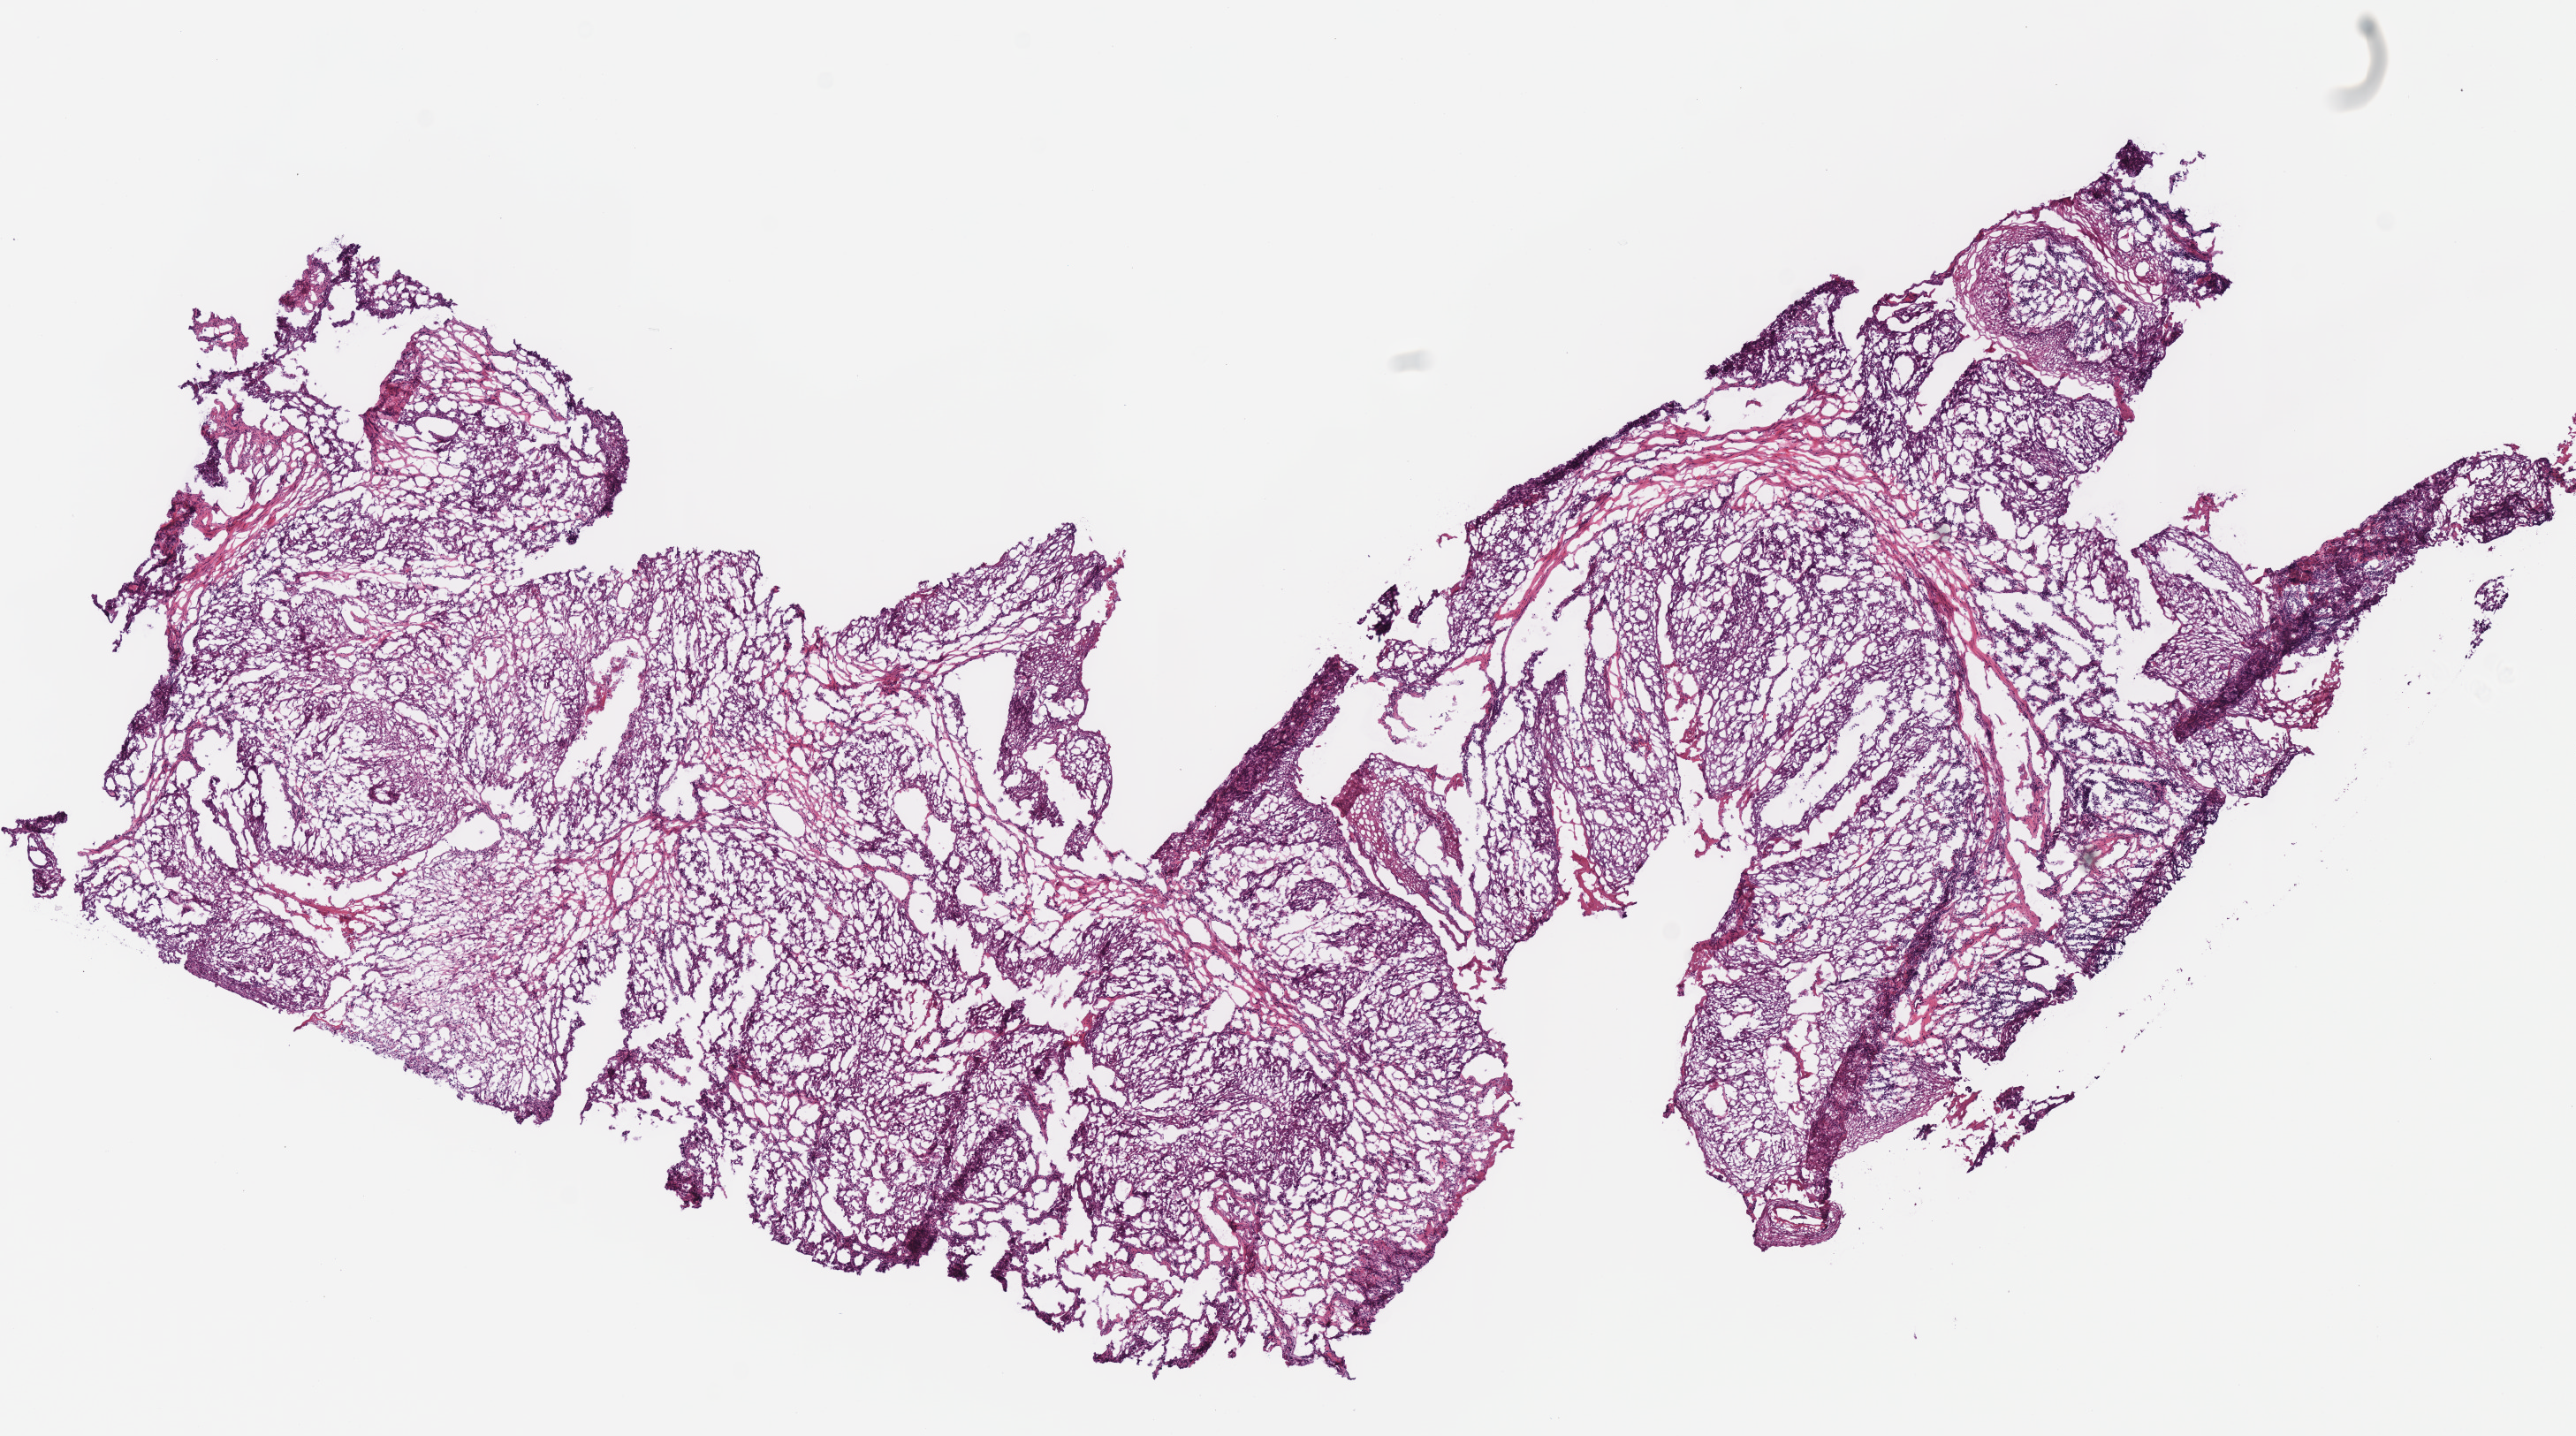
Whole-slide histology image, H&E-stained, a low-resolution overview of the entire scanned area, about 11.5 x 6.4 mm (slide scanned at 40x), frozen section from the bottom of the tissue portion, sample: primary tumour, head and neck. Male patient; age at initial diagnosis 65 years. Histologic grade: G3 (poorly differentiated). Composition of this section per pathologist review: tumour cells 85%, tumour nuclei 71%, normal cells 15%, stromal cells 0%, necrosis 0%. Inflammatory infiltration, as recorded: lymphocyte infiltration 10%, monocyte infiltration 5%, neutrophil infiltration 5%.
* pathologic diagnosis: Squamous cell carcinoma, NOS (overlapping lesion of lip, oral cavity and pharynx)